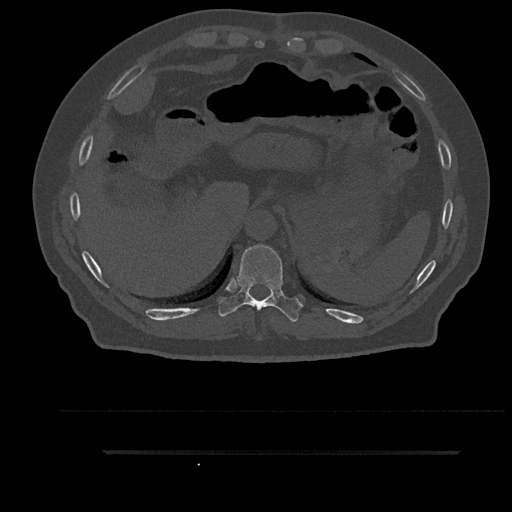
CT including the spine, one axial slice. Slice 374 of 797 in the series (ordered by position). Reconstruction kernel Br40s/3. Bone window (W 1800 / L 400 HU). 512 × 512 image matrix, field of view 432 × 432 mm. Patient: male, 63 years. From the clinical record (not read from this slice): primary cancer: renal.
Structures marked on this image (semi-automatic segmentation, software-assisted and operator-edited):
- T10 vertebra: bounding box [x1, y1, x2, y2] px = [218, 245, 303, 322]